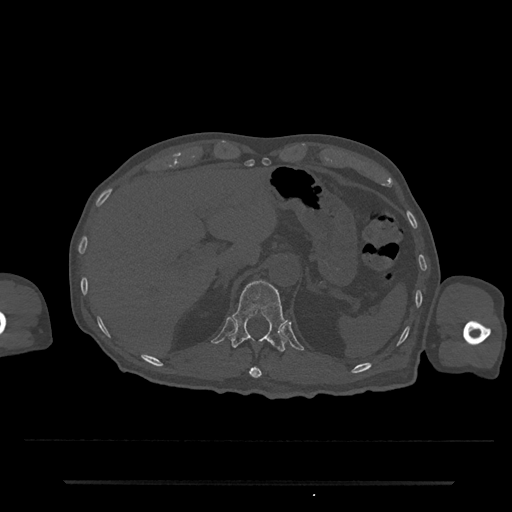
CT including the spine, one axial slice; position 206 of 797 along the scan axis; reconstruction kernel Br40s/3; bone window (W 1800 / L 400 HU); 0.5 mm slice thickness; 512 × 512 image matrix. Male patient, age 74 years. From the clinical record (not read from this slice): primary cancer: prostate.
Structures marked on this image (semi-automatically segmented with operator editing):
- T11 vertebra: bounding box (x1, y1, x2, y2) in pixels: (249, 366, 262, 378)
- T12 vertebra: (229, 280, 287, 352)